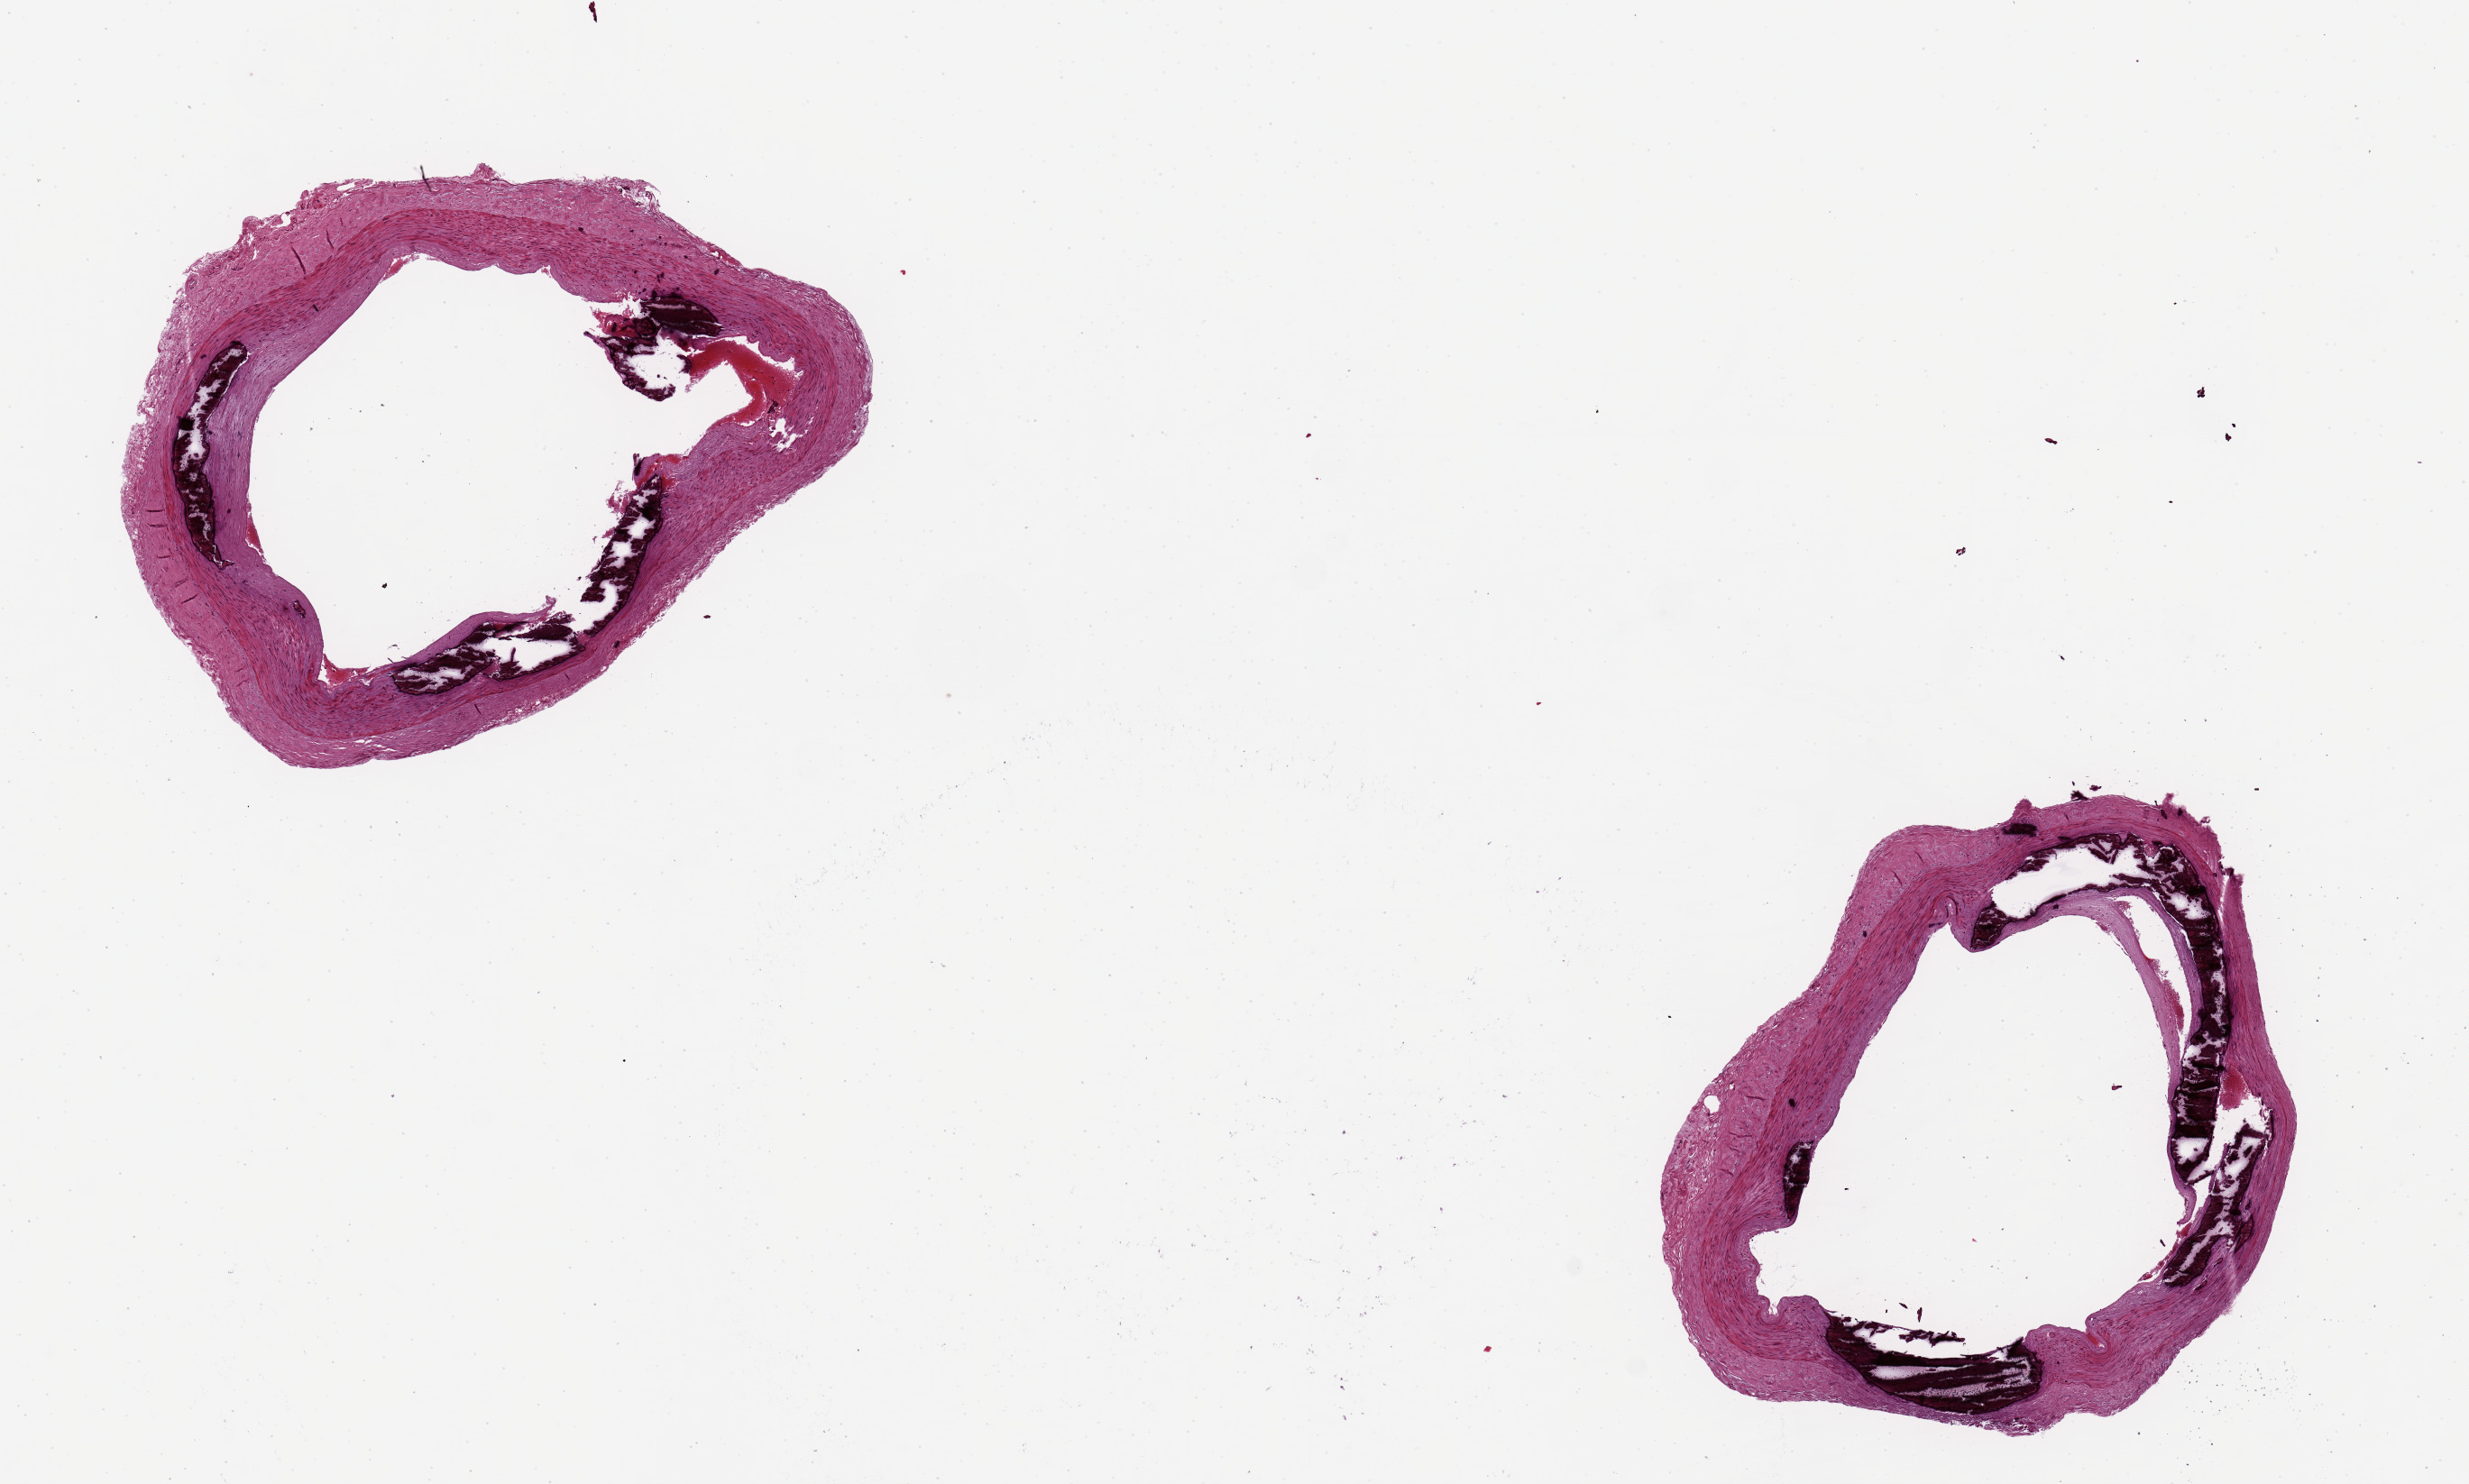
Whole-slide image, hematoxylin and eosin (H&E) stain, shown as a low-resolution overview of the whole scanned area (about 10.8 x 6.5 mm, slide scanned at 20x); PAXgene-fixed paraffin-embedded (PFPE) section; section of tibial artery (target tissue); tissue donor sample. Male donor.
Review note (as recorded): 2 pieces, both with severely caclified partially occlusive atherosclerosis 2.5mm d.